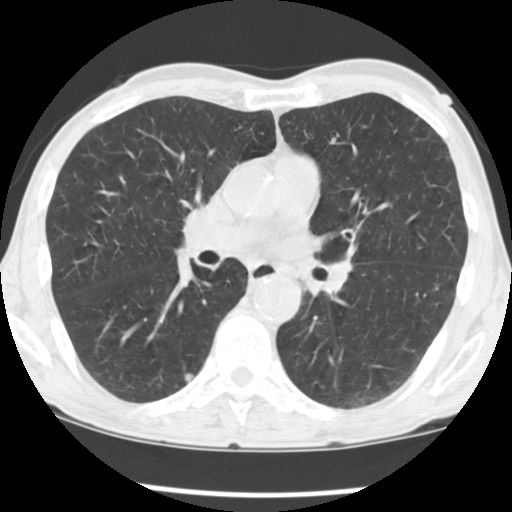
Chest CT (low-dose screening protocol), one axial image; baseline screening round; lung window (W 1500 / L -600 HU); 2.5 mm slice thickness; 120 kVp; slice 65 of 135 in the series; 512 × 512 image matrix. Male participant, aged 68 years at enrolment. Current smoker at enrolment.
Expert reader's lesion annotation, bounding box (x1, y1, x2, y2) in pixels: (169, 361, 209, 400). The screening reader recorded 4 non-calcified nodules or masses ≥4 mm on this exam (right middle lobe, left upper lobe, right lower lobe, right lower lobe); which of them this box marks is not recorded. Official screen result: positive, change unspecified: nodule(s) >= 4 mm or enlarging nodule(s), mass(es), or other non-specific abnormalities suspicious for lung cancer. Participant outcome: lung cancer diagnosed 284 days after this screen — adenocarcinoma, NOS, right lower lobe, moderately differentiated (G2), stage IV (AJCC 6th edition), 14 mm at pathology.